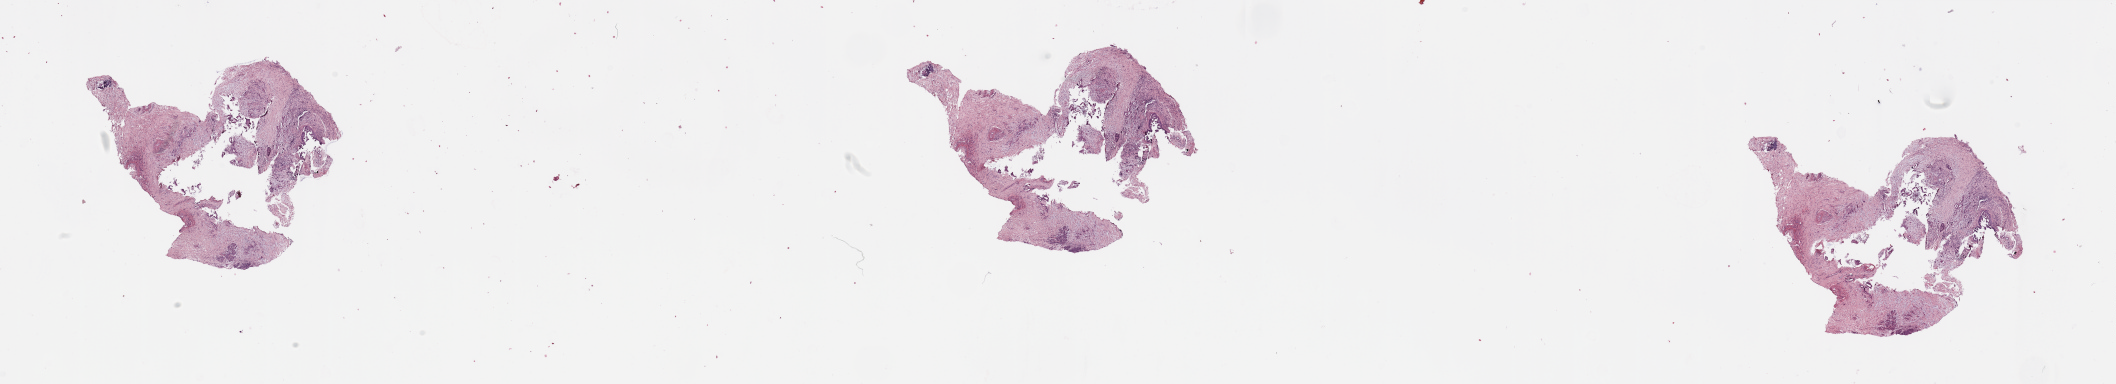
Whole-slide histology image, H&E-stained, shown as a low-resolution overview of the whole scanned area (about 33.5 x 6.1 mm, acquisition: 20x scan); tumour tissue sample, sampled site: pancreas. Patient: male, age 65 years. Histologic grade: G2 (moderately differentiated). Composition of this section per pathologist review: tumour nuclei 10%, necrosis 0%.
AJCC pathologic stage: IV. Diagnosis: Infiltrating duct carcinoma, NOS. Primary tumour site (as recorded): head.